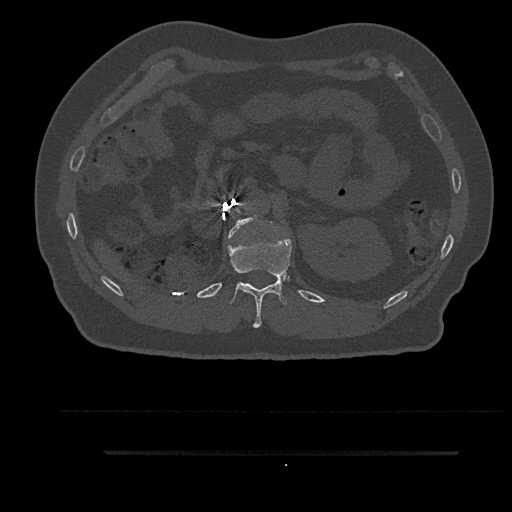
CT including the spine, one axial slice; position 228 of 797 along the scan axis; 120 kVp; bone window (W 1800 / L 400 HU); 0.5 mm slice thickness; 512 × 512 image matrix, field of view 432 × 432 mm. Male patient, age 63 years. From the clinical record (not read from this slice): primary cancer: renal; vertebrae with lytic lesions (as recorded): T8.
Structures marked on this image (semi-automatically segmented with operator editing):
- L1 vertebra: bounding box <228,216,257,238> (left, top, right, bottom; pixels)
- T12 vertebra: <227,230,292,328>